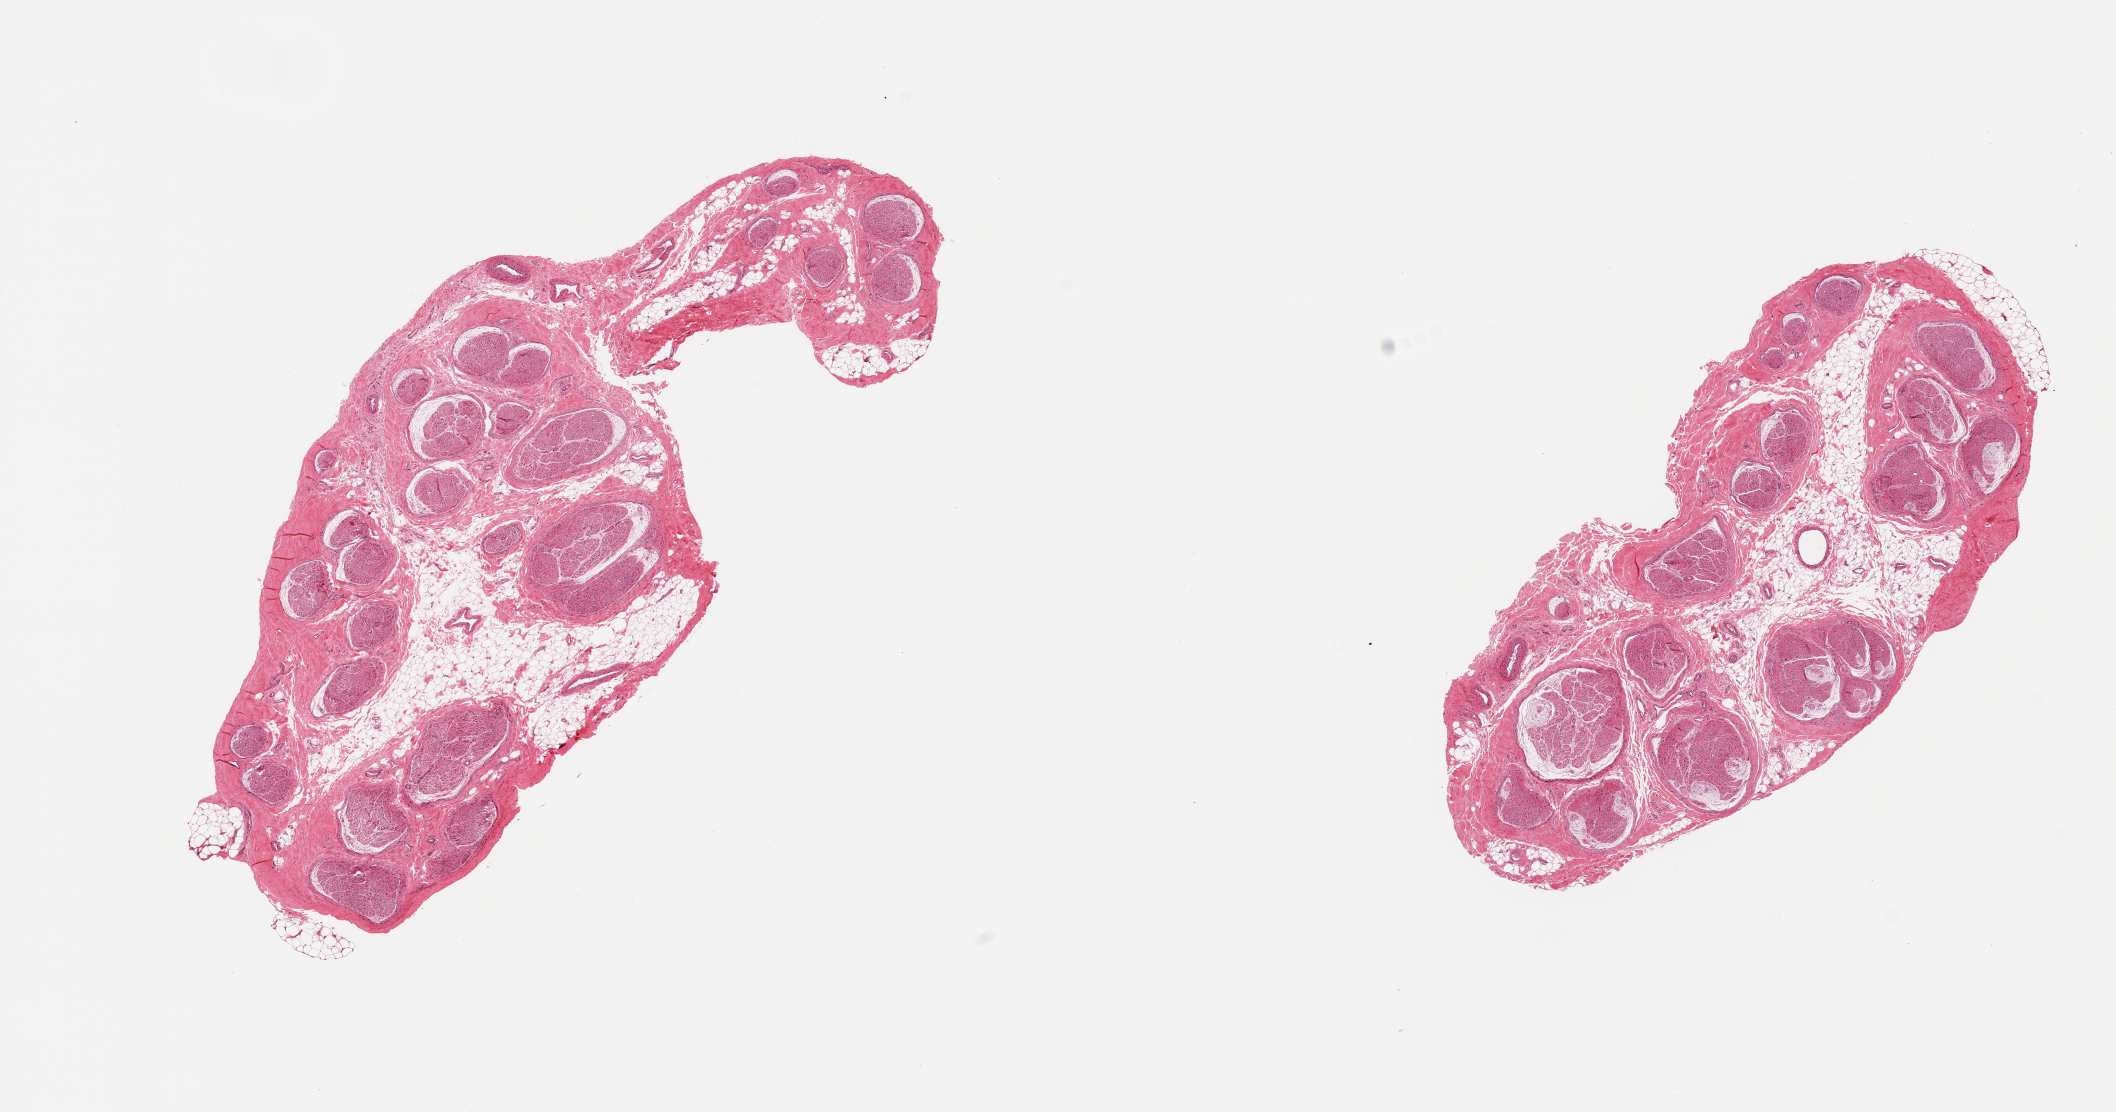
H&E whole-slide image, shown as a low-resolution overview of the whole scanned area (about 16.7 x 8.8 mm, from a 20x scan), PAXgene-fixed, paraffin-embedded tissue, section of tibial nerve (target tissue), donor tissue sample. Male donor.
Review note (as recorded): 2 pieces; ~20% internal fat.